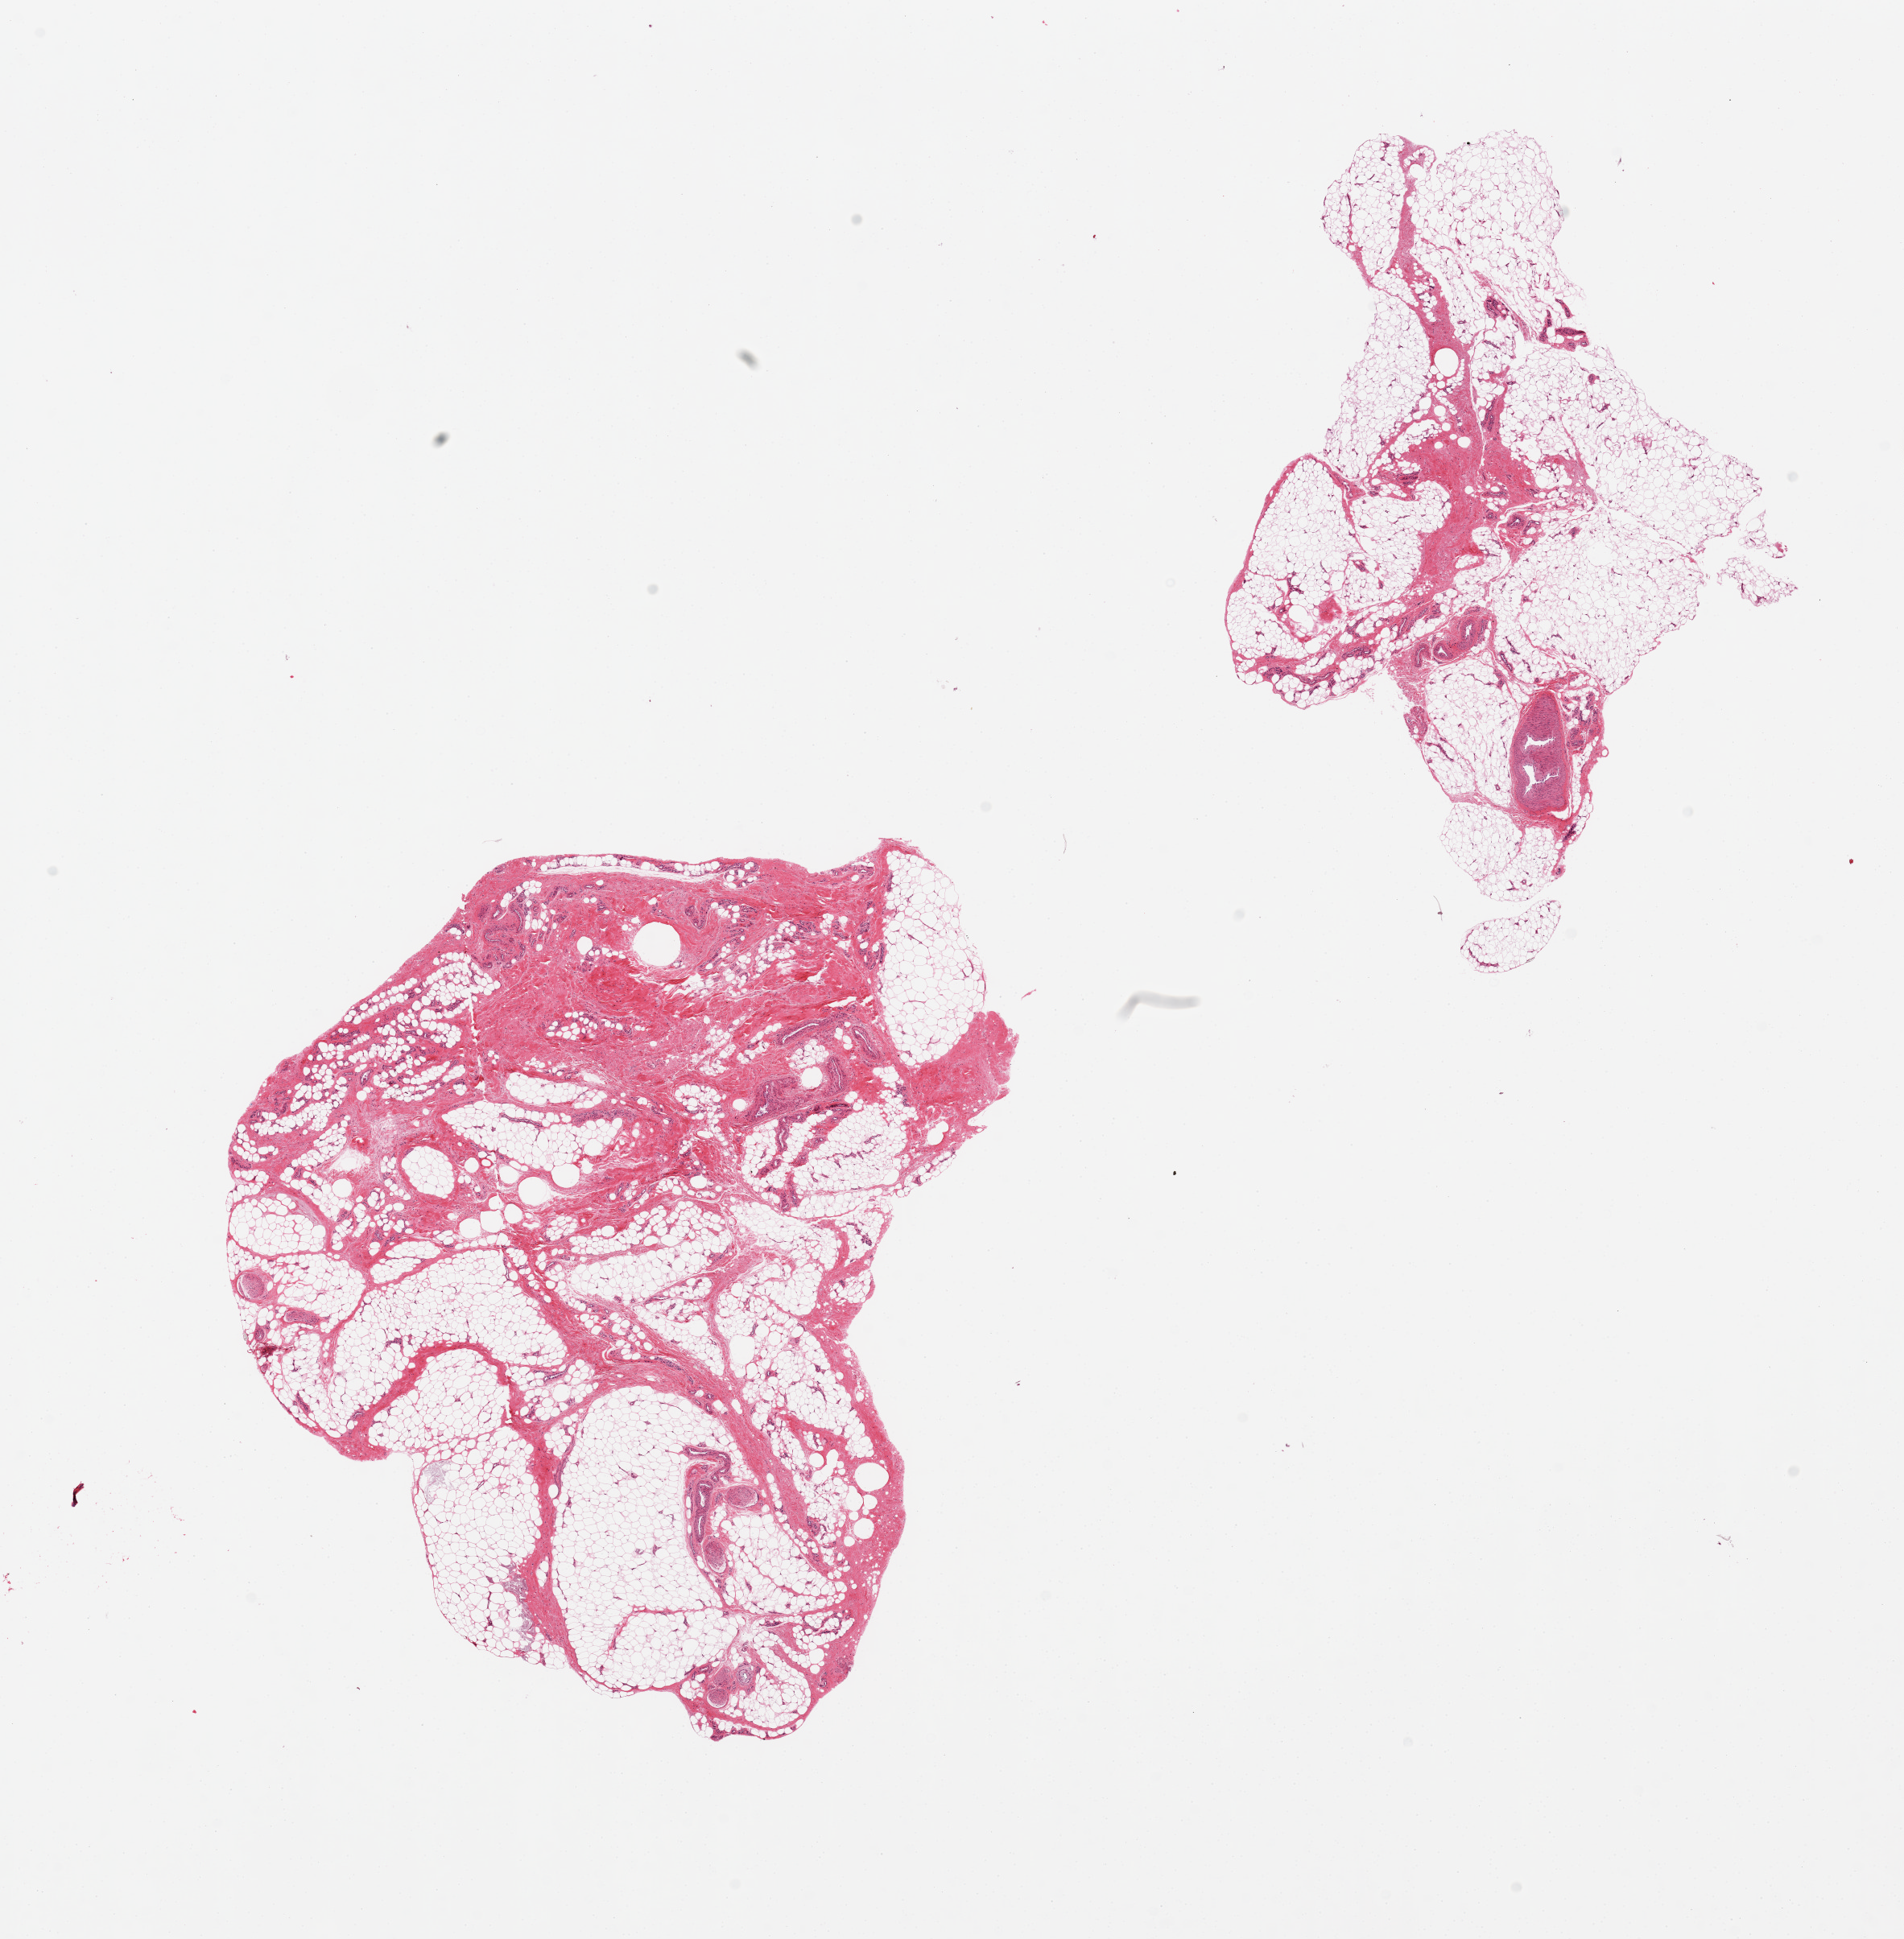
Whole-slide image, haematoxylin and eosin stain, brightfield, whole scanned area (about 18.7 x 19.1 mm, slide scanned at 20x) shown as a low-resolution overview, PAXgene-fixed, paraffin-embedded tissue, section of adipose tissue (target tissue), tissue donor sample. Male donor.
Reviewer comment on this tissue sample: 2 pieces, larger piece is 30% fibrovascular tissue and nerve, smaller piece ~10%.